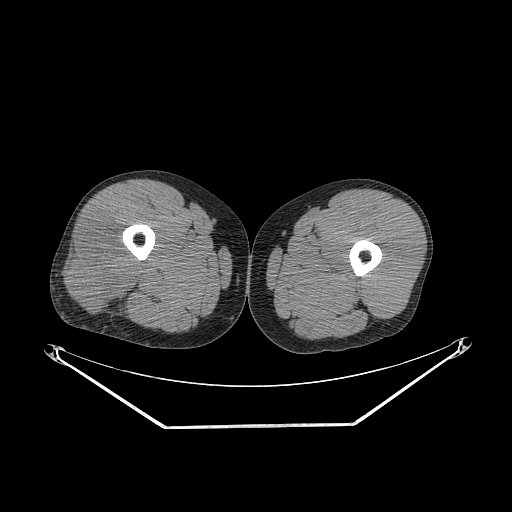
CT of an extremity soft-tissue mass (from a PET/CT study), one axial slice. Position 245 of 267 along the scan axis. 140 kVp. Soft-tissue window (W 400 / L 40 HU). 512 × 512 image matrix, field of view 500 × 500 mm. Male patient. From the clinical record (not read from this slice): histological type: poorly differentiated synovial sarcoma; grade: high; site of the primary tumour: right buttock.
Outlined on this slice (expert contour drawn on MRI and transferred to this co-registered scan by the dataset authors):
- gross tumour volume including surrounding oedema: bounding box (x1, y1, x2, y2) in pixels: (69, 221, 138, 309)
- gross tumour volume (mass): (71, 221, 138, 307)